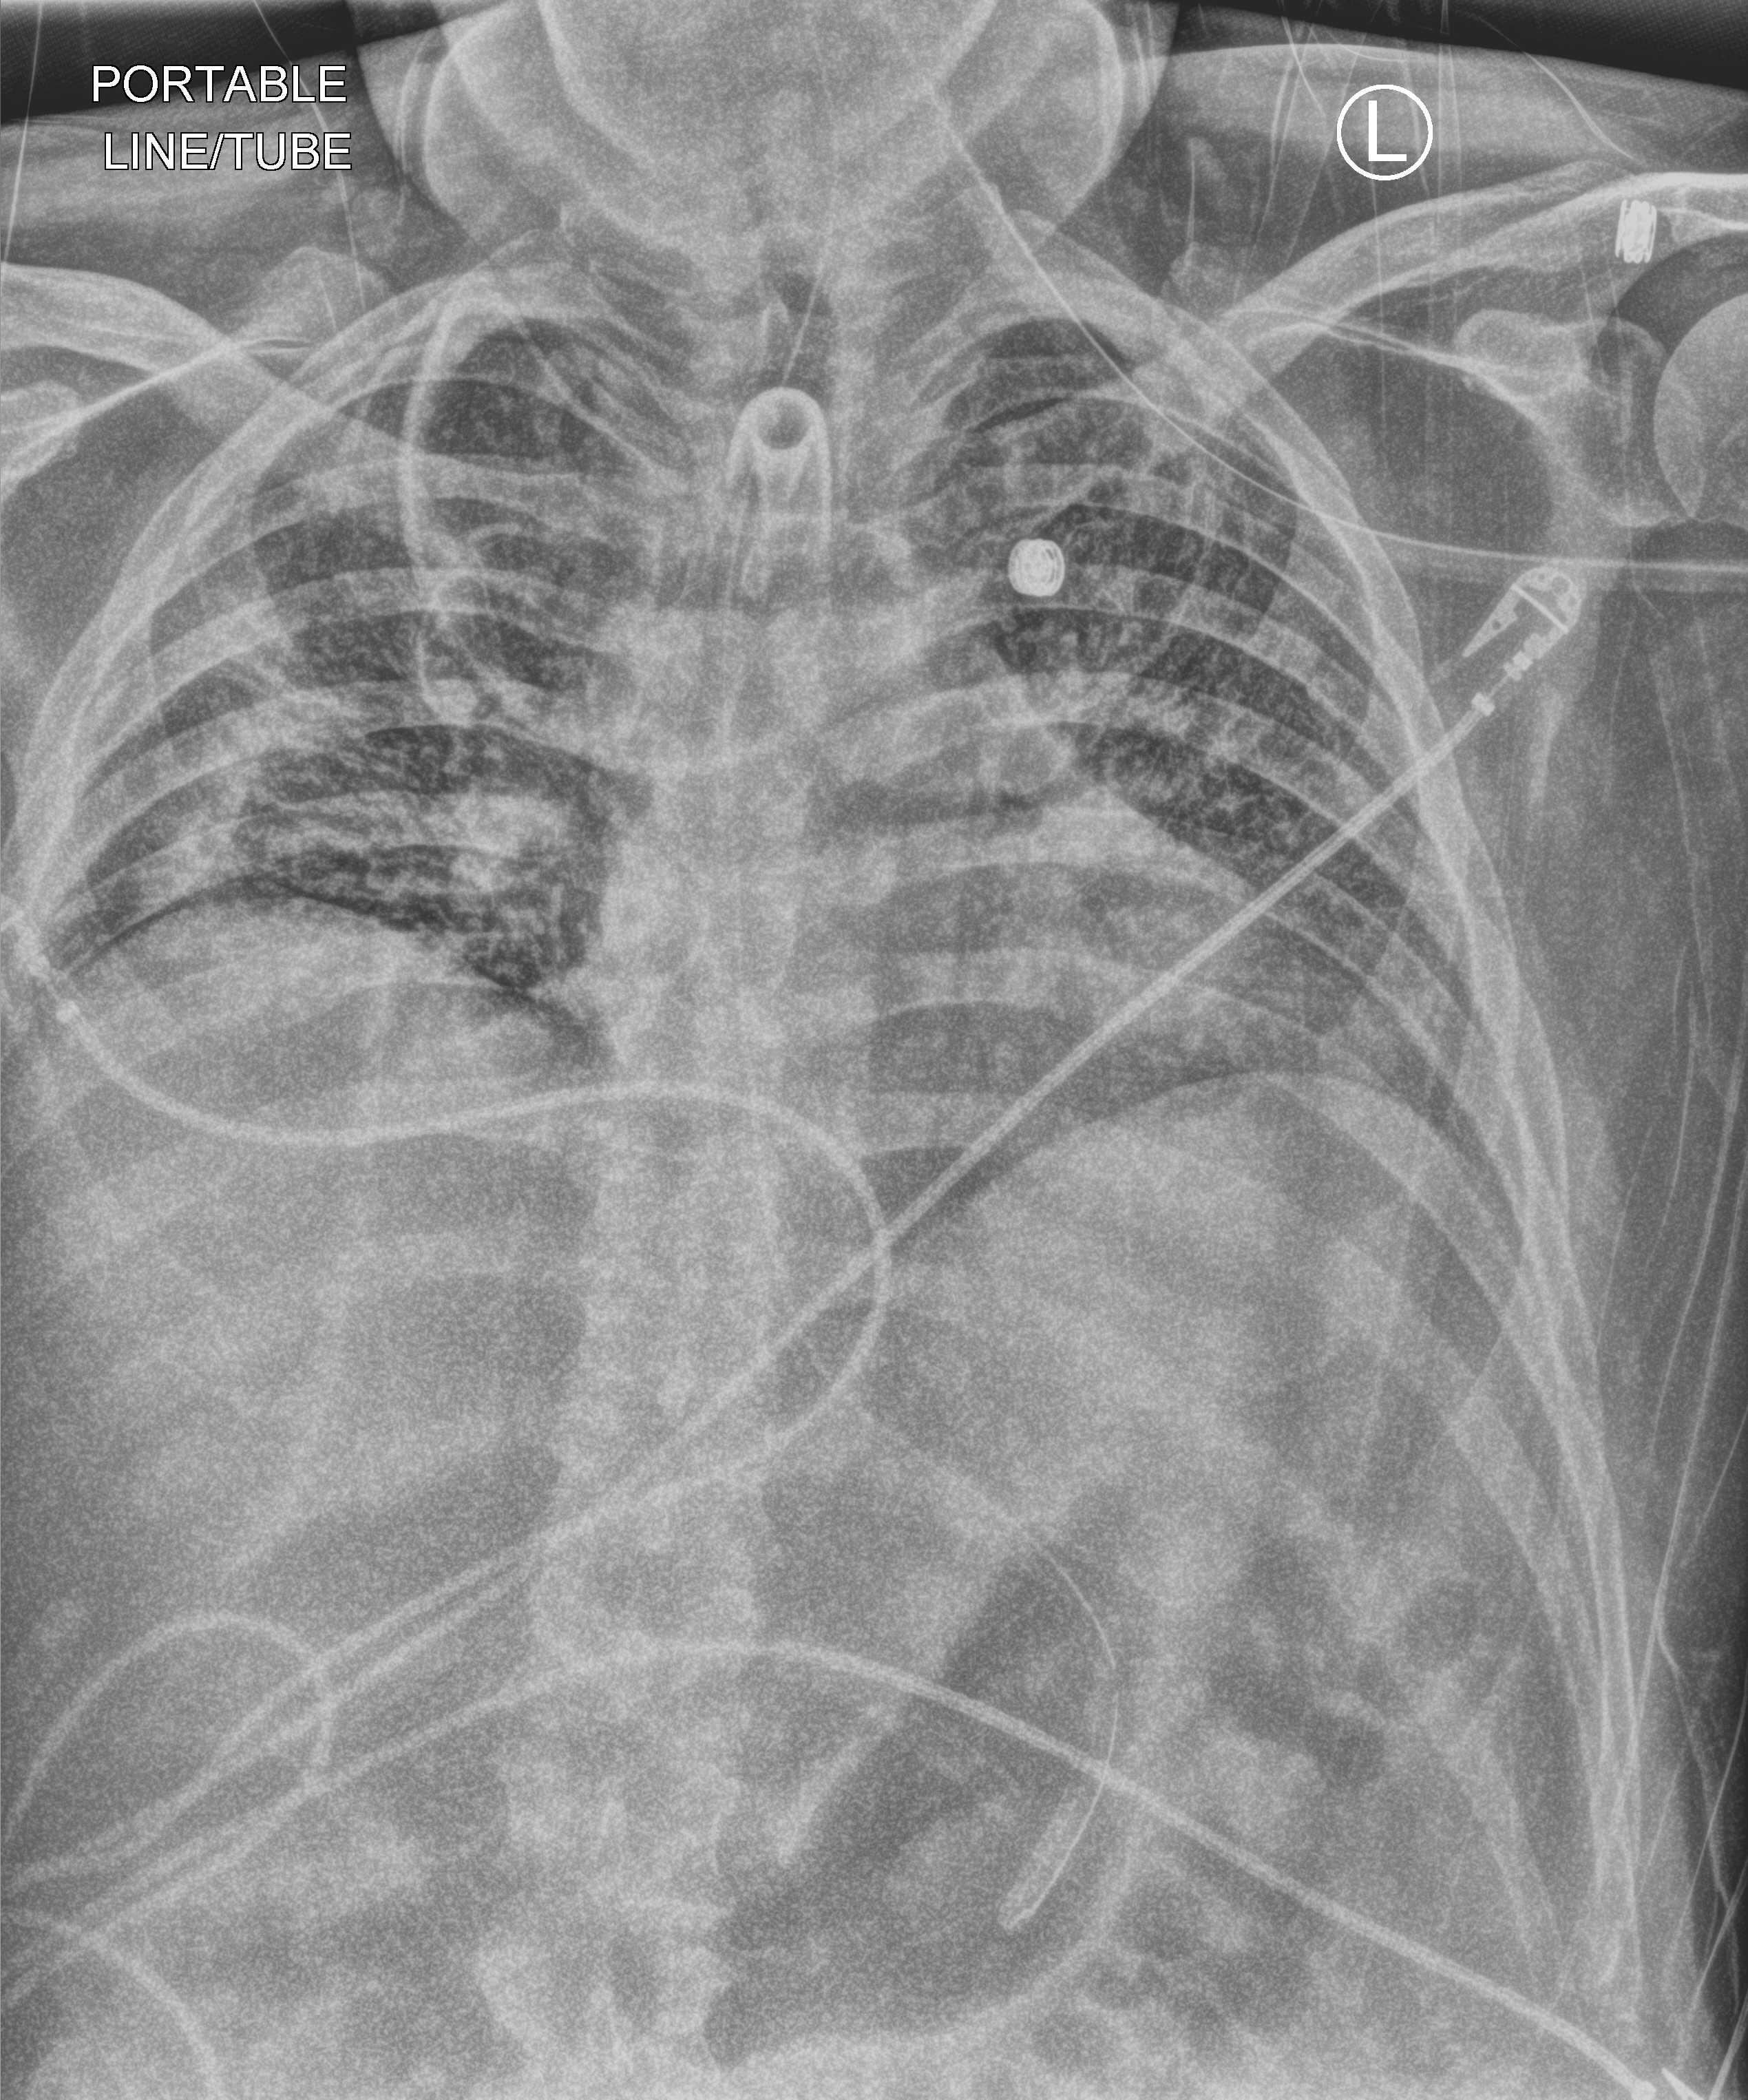
Chest X-ray (portable); anteroposterior (AP) projection. Patient hospitalised with COVID-19; male, aged 18–59 years.
Hospital-stay facts (about this admission, not read from this image; timing relative to this image not recorded): mechanically ventilated during this hospital stay: yes; admitted to intensive care during this hospital stay: yes.